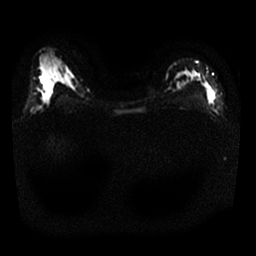
Breast MRI, one axial slice. Slice 18 of 25 in the series (ordered by position). Diffusion-weighted series; image 2 of 4 stored at this slice position (different b-values; order by instance number). 1.5 T. 4 mm slice thickness. 256 × 256 image matrix, field of view 320 × 320 mm. Female patient.
Structures marked on this image (expert manual segmentation):
- tumour on diffusion-weighted imaging: bounding box <207,92,211,96> (left, top, right, bottom; pixels)